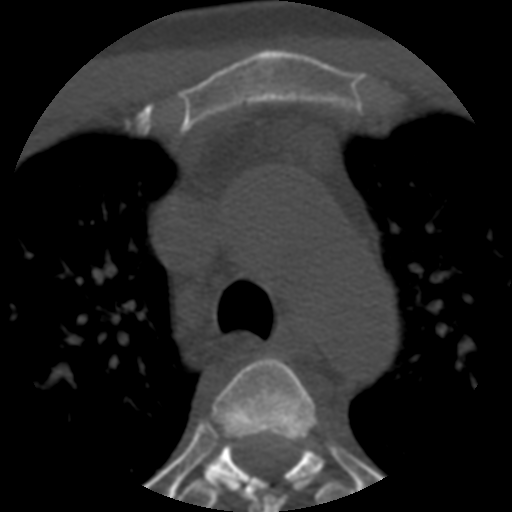
CT including the spine, one axial slice; slice 405 of 508 in the series (ordered by position); bone window (W 1800 / L 400 HU); 1.25 mm slice thickness; 512 × 512 image matrix, field of view 160 × 160 mm. Patient age 57 years. From the clinical record (not read from this slice): primary cancer: prostate.
Structures marked on this image (semi-automatically segmented with operator editing):
- T3 vertebra: bounding box <211,357,317,512> (left, top, right, bottom; pixels)
- T4 vertebra: <177,427,360,509>